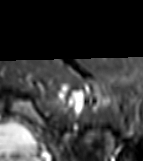
MRI of an extremity soft-tissue mass, one axial slice; position 61 of 81 along the scan axis; STIR; MR volume resampled by the dataset authors to the PET/CT grid (not the native acquisition matrix); 3.27 mm slice thickness; 143 × 161 image matrix, field of view 140 × 157 mm. Female patient. From the clinical record (not read from this slice): histological type: myxofibrosarcoma; grade: intermediate; site of the primary tumour: left thigh.
Outlined on this slice (expert contour drawn on MRI and transferred to this co-registered scan by the dataset authors):
- gross tumour volume including surrounding oedema: bounding box [x1, y1, x2, y2] px = [65, 85, 89, 107]